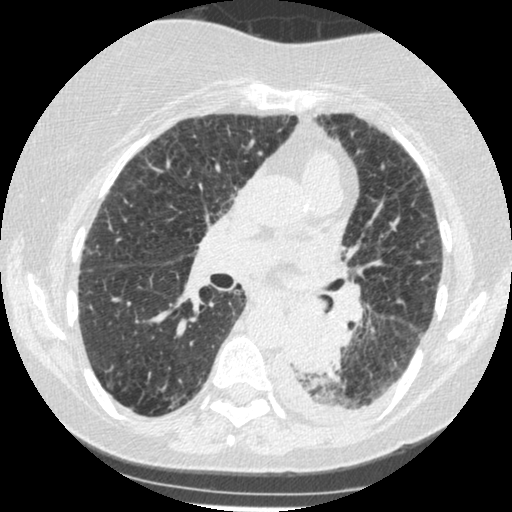
Low-dose screening chest CT, one axial slice. Slice 137 of 341 in the series (ordered by position). 120 kVp. Lung window (W 1500 / L -600 HU). 512 × 512 image matrix, field of view 310 × 310 mm.
Annotated regions visible in this slice (outlined manually by an expert reader):
- lesion 1 (tumor, lower lobe of left lung): bounding box (x1, y1, x2, y2) in pixels: (285, 309, 340, 374)